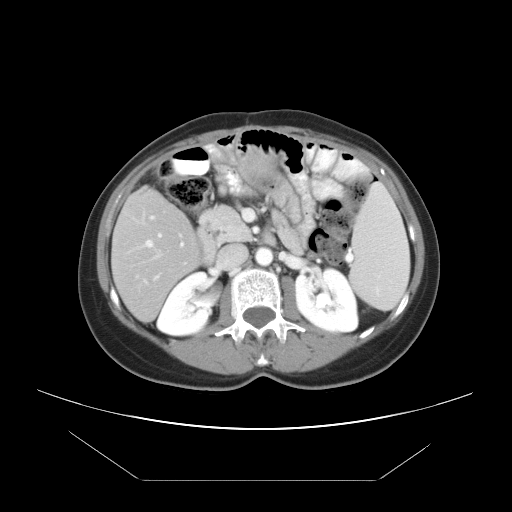
Contrast-enhanced abdominal CT, one axial slice; position 19 of 45 along the scan axis; reconstruction kernel STANDARD; intravenous contrast given; soft-tissue window (W 400 / L 40 HU); 512 × 512 image matrix, field of view 405 × 405 mm. Female patient, age 52 years. From the clinical record (not read from this slice): diagnosis: colorectal cancer liver metastases, imaged before liver resection; multiple liver metastases: yes; largest metastasis: 2.5 cm.
Outlined on this slice (expert manual segmentation):
- hepatic veins: box from (x=146, y=234) to (x=161, y=278) px
- liver: (x=112, y=190)–(x=199, y=320)
- planned liver remnant (the part of the liver to remain after resection): (x=112, y=190)–(x=197, y=317)
- portal vein (with intrahepatic branches): (x=149, y=216)–(x=184, y=259)